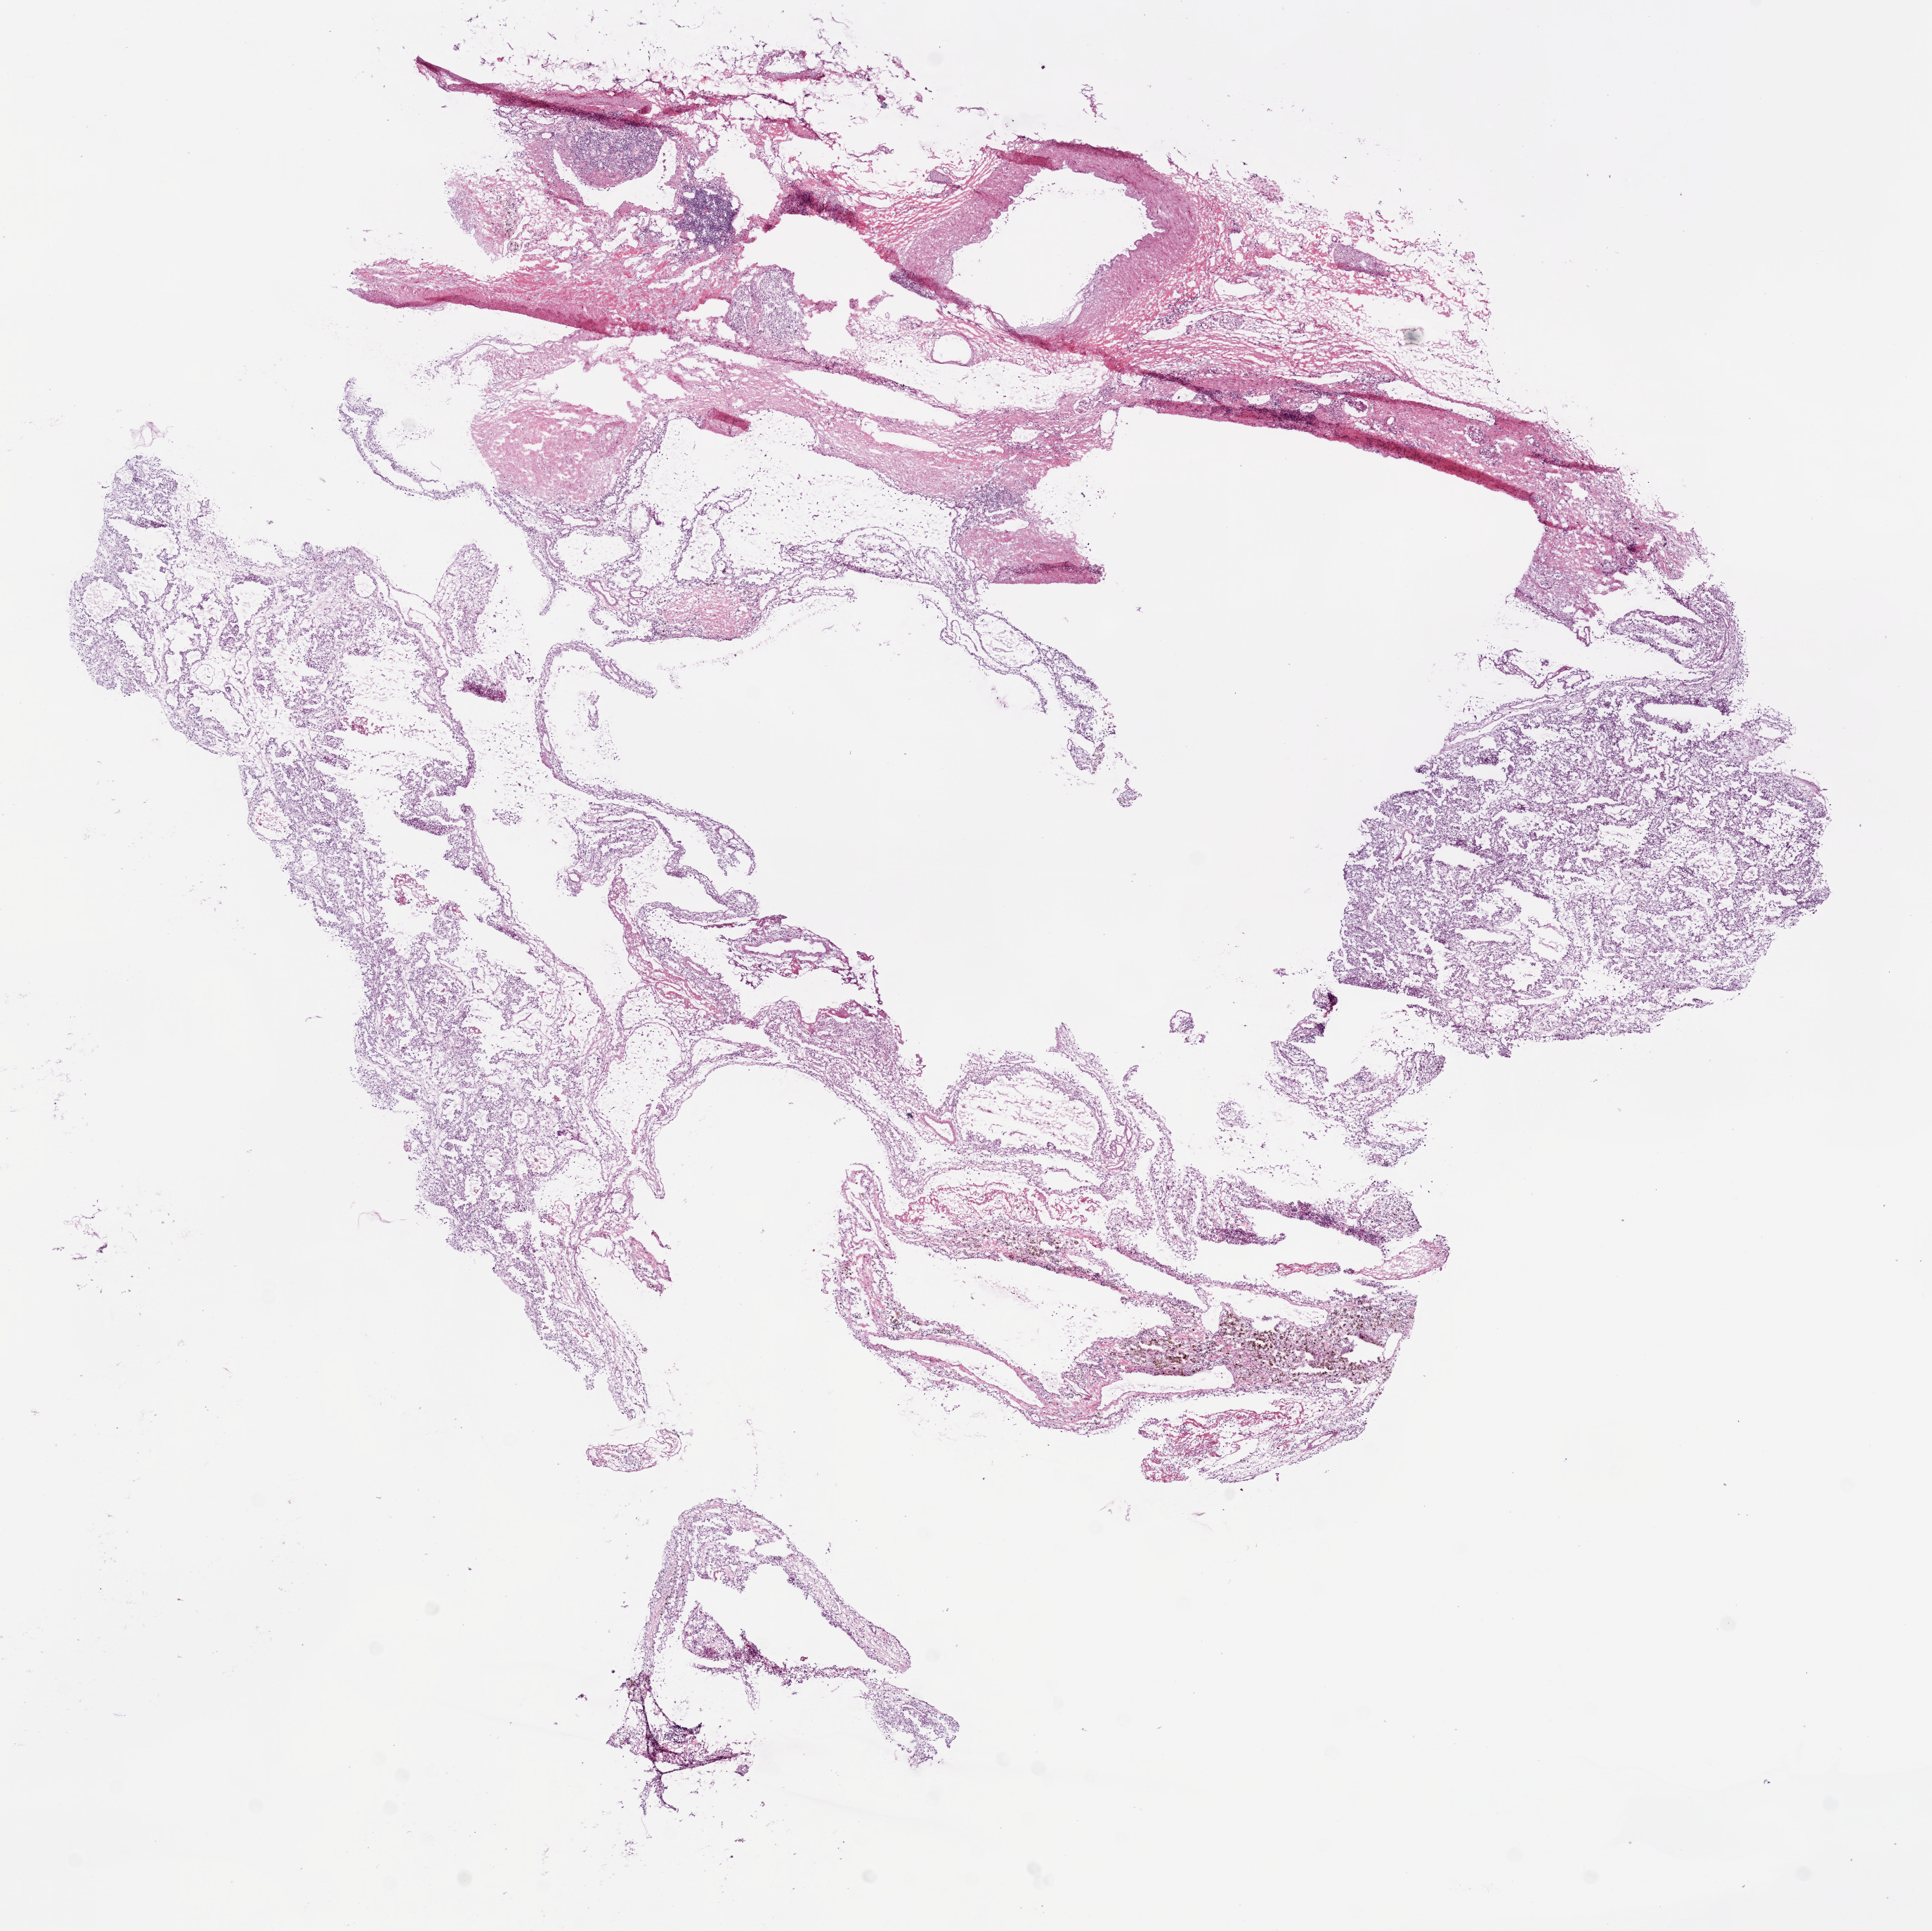
H&E-stained whole-slide image, a low-resolution overview of the entire scanned area, about 11.0 x 11.0 mm (slide scanned at 20x); frozen section from the bottom of the tissue portion; primary tumour sample from the kidney. Male, age 46 years at initial diagnosis. Histologic grade: G2 (moderately differentiated). Slide review estimates, as recorded: tumour cells 80%, tumour nuclei 75%, normal cells 10%, stromal cells 10%, necrosis 0%.
AJCC pathologic stage: I. Diagnosis: Clear cell adenocarcinoma, NOS.